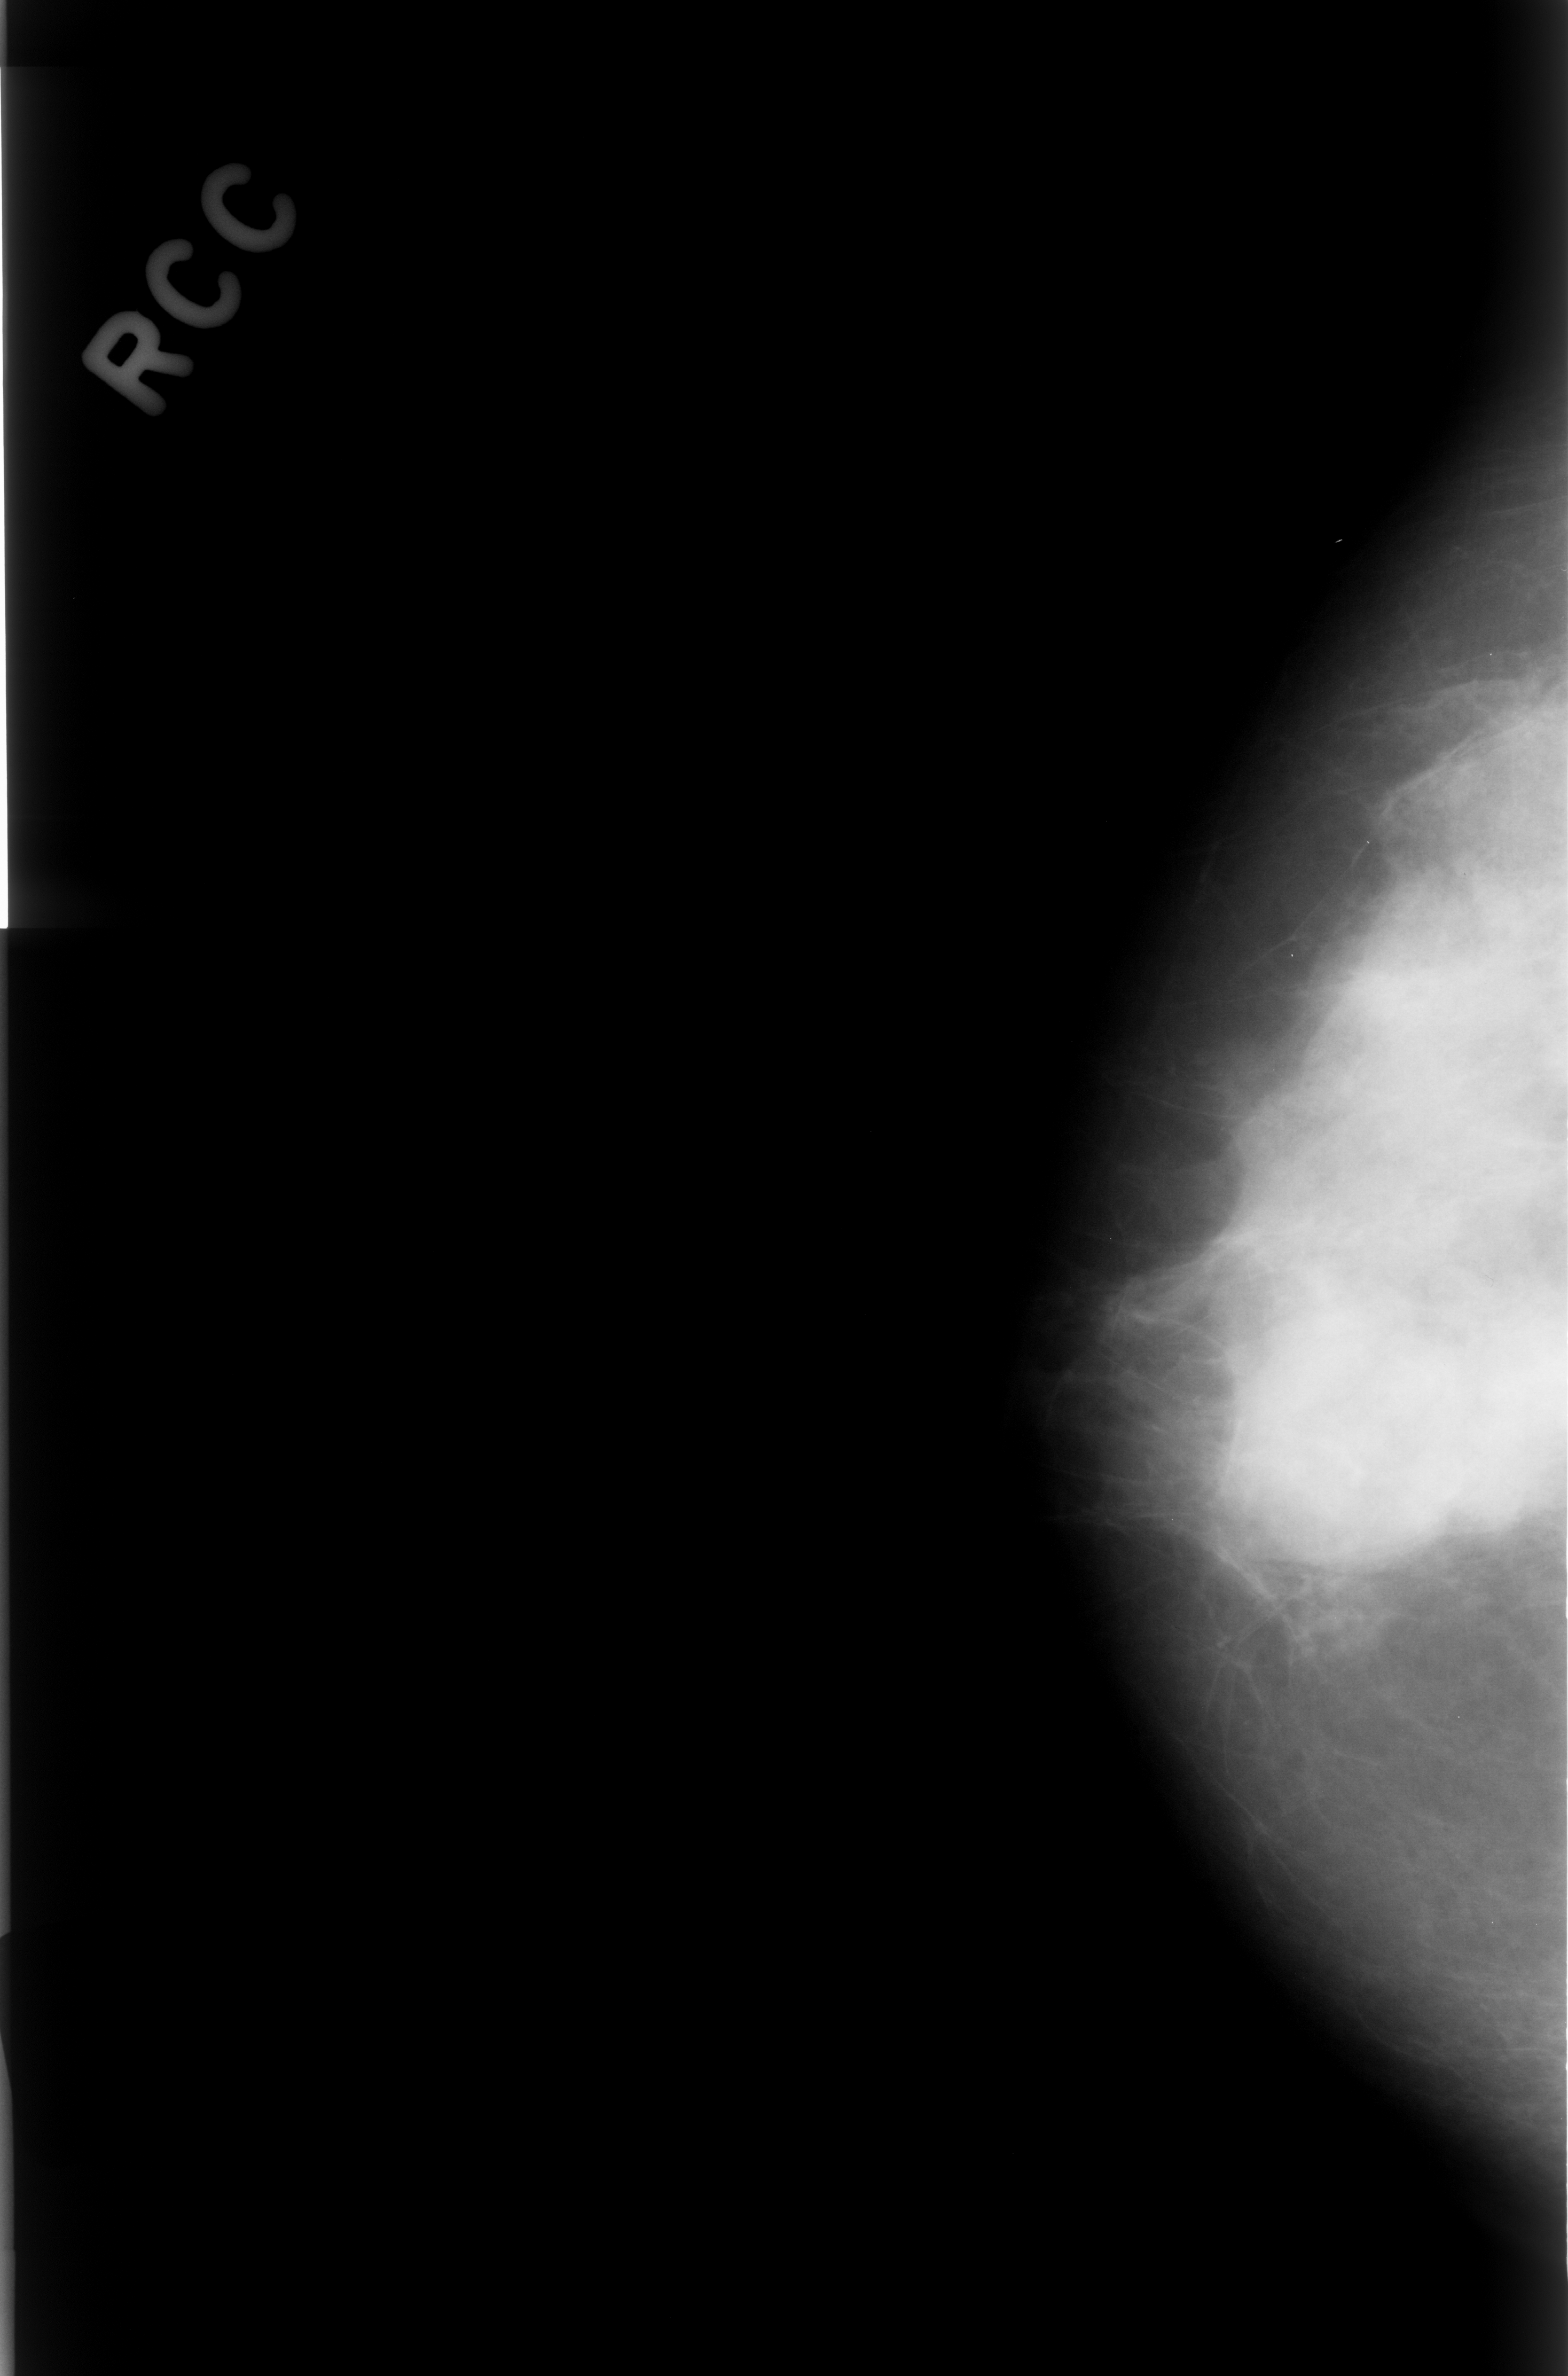
Mammogram (digitized film), right breast, CC view.
Radiologist-marked abnormalities on this image: mass, shape lobulated, margins obscured; BI-RADS assessment category 3; subtlety rating 4 on a 1 (subtle) to 5 (obvious) scale; pathology result (as recorded, not read from the image): benign.